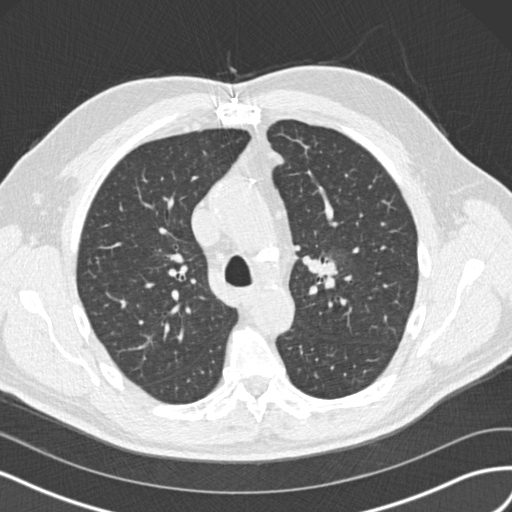
Axial slice from a low-dose chest CT screening exam. Baseline screening round. Lung window (W 1500 / L -600 HU). 2 mm slice thickness. Slice 50 of 160 in the series. Male, age 65 years at enrolment. Former smoker at enrolment.
Expert reader's lesion annotation, box from (x=297, y=243) to (x=354, y=297) px. The screening reader recorded 4 non-calcified nodules or masses ≥4 mm on this exam; which of them this box marks is not recorded. Later outcome: lung cancer diagnosed 945 days after this screen — acinar cell carcinoma, left upper lobe, stage IA (AJCC 6th edition), 25 mm at pathology.